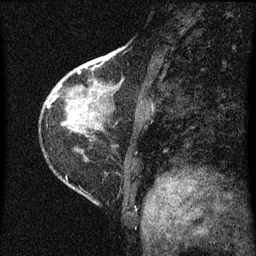
Breast MRI (dynamic contrast-enhanced), one sagittal slice. Slice 20 of 60 in the series (ordered by position). Dynamic contrast-enhanced series, image 2 of 3 at this slice position (ordered by acquisition). 1.5 T. TE 4.2 ms, TR 8 ms. 256 × 256 image matrix. Patient: female, 38 years.
Annotated regions visible in this slice (semi-automatically segmented with operator editing):
- analysis volume of interest (the breast-tissue region the enhancement analysis was run in; not a lesion): bounding box (x1, y1, x2, y2) in pixels: (67, 44, 144, 131)
- tumour enhancement mask (voxels above the 70 % enhancement threshold inside the analysis volume of interest): (77, 72, 81, 73)